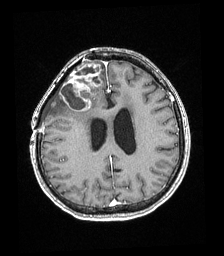
Brain MRI from a brain-tumour surgery series, one axial slice; T1-weighted post-contrast; 1 mm slice thickness; 224 × 256 image matrix. From the clinical record (not read from this slice): histopathology: Astrocytoma; WHO grade: 4; IDH mutation: yes; tumour location: Right superficial frontal.
Annotated regions visible in this slice (expert manual segmentation):
- tumour: bounding box [x1, y1, x2, y2] px = [60, 62, 102, 112]